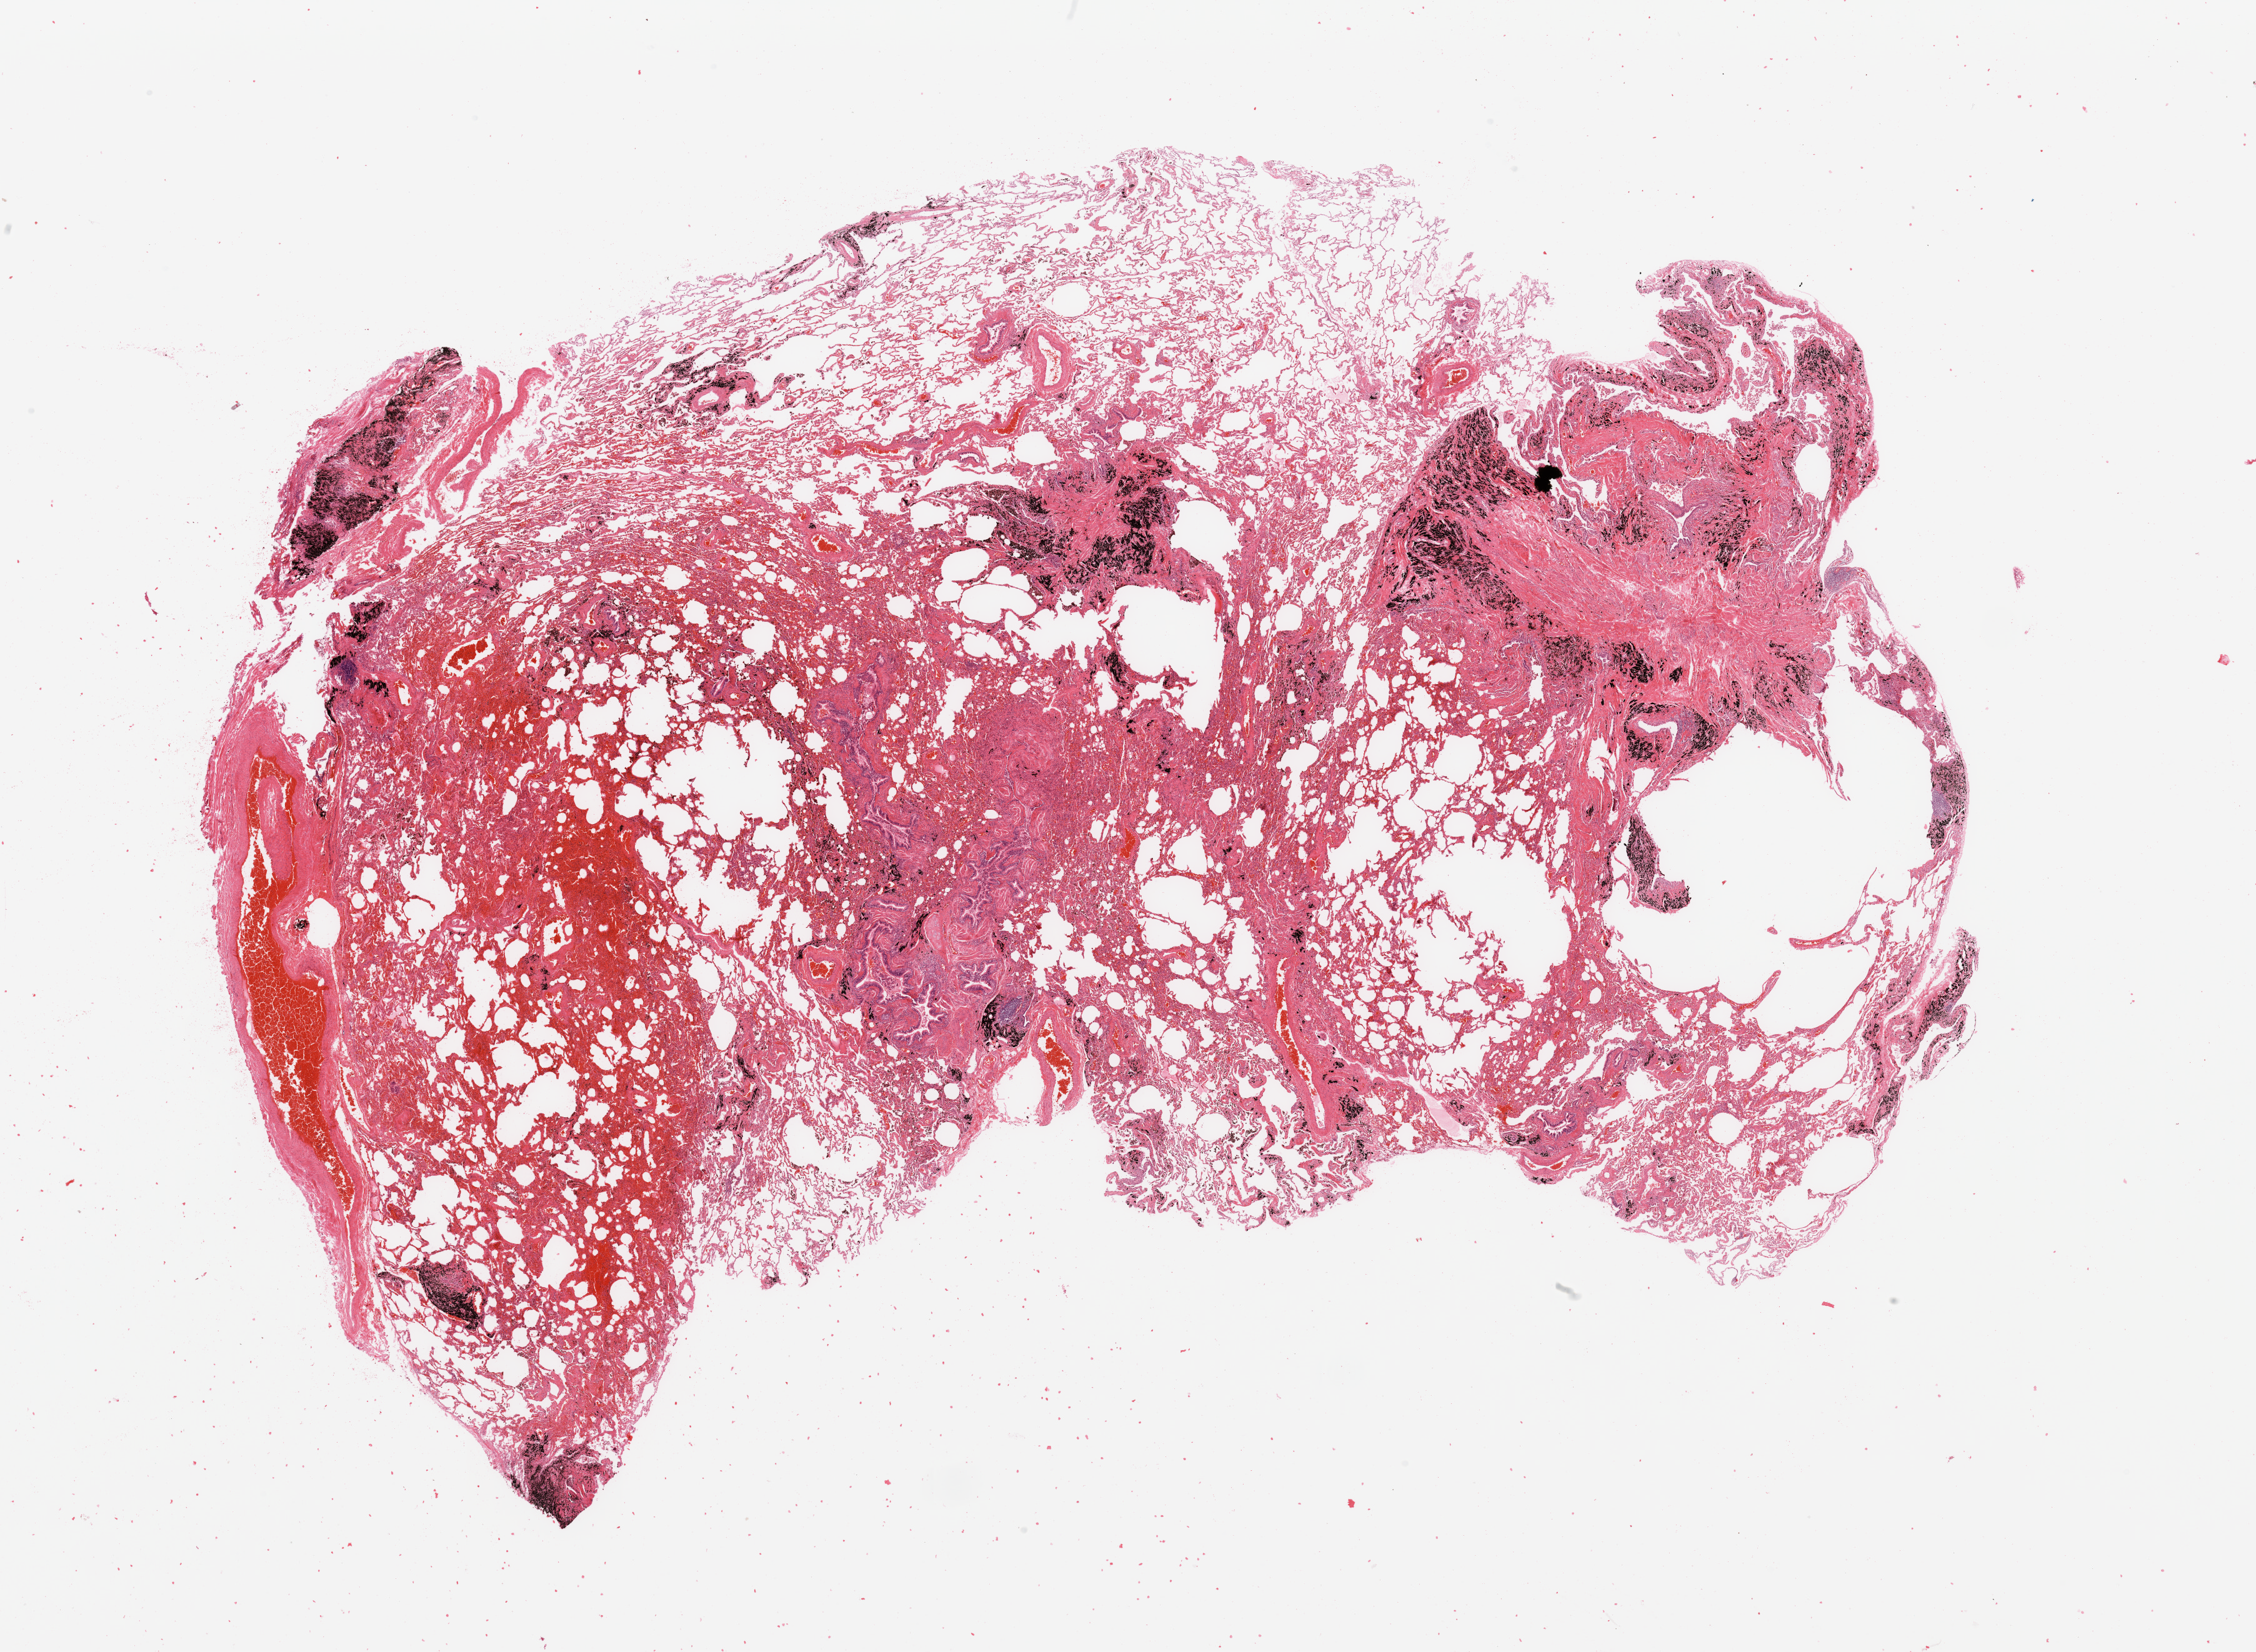
Whole-slide histology image, H&E, a low-resolution overview of the entire scanned area, about 28.5 x 20.9 mm. Normal (non-tumour) tissue sample, sampled site: lung. Patient: male, age 56 years.
This section: normal (non-tumour) tissue from the same patient. Patient diagnosis: Adenocarcinoma, NOS.